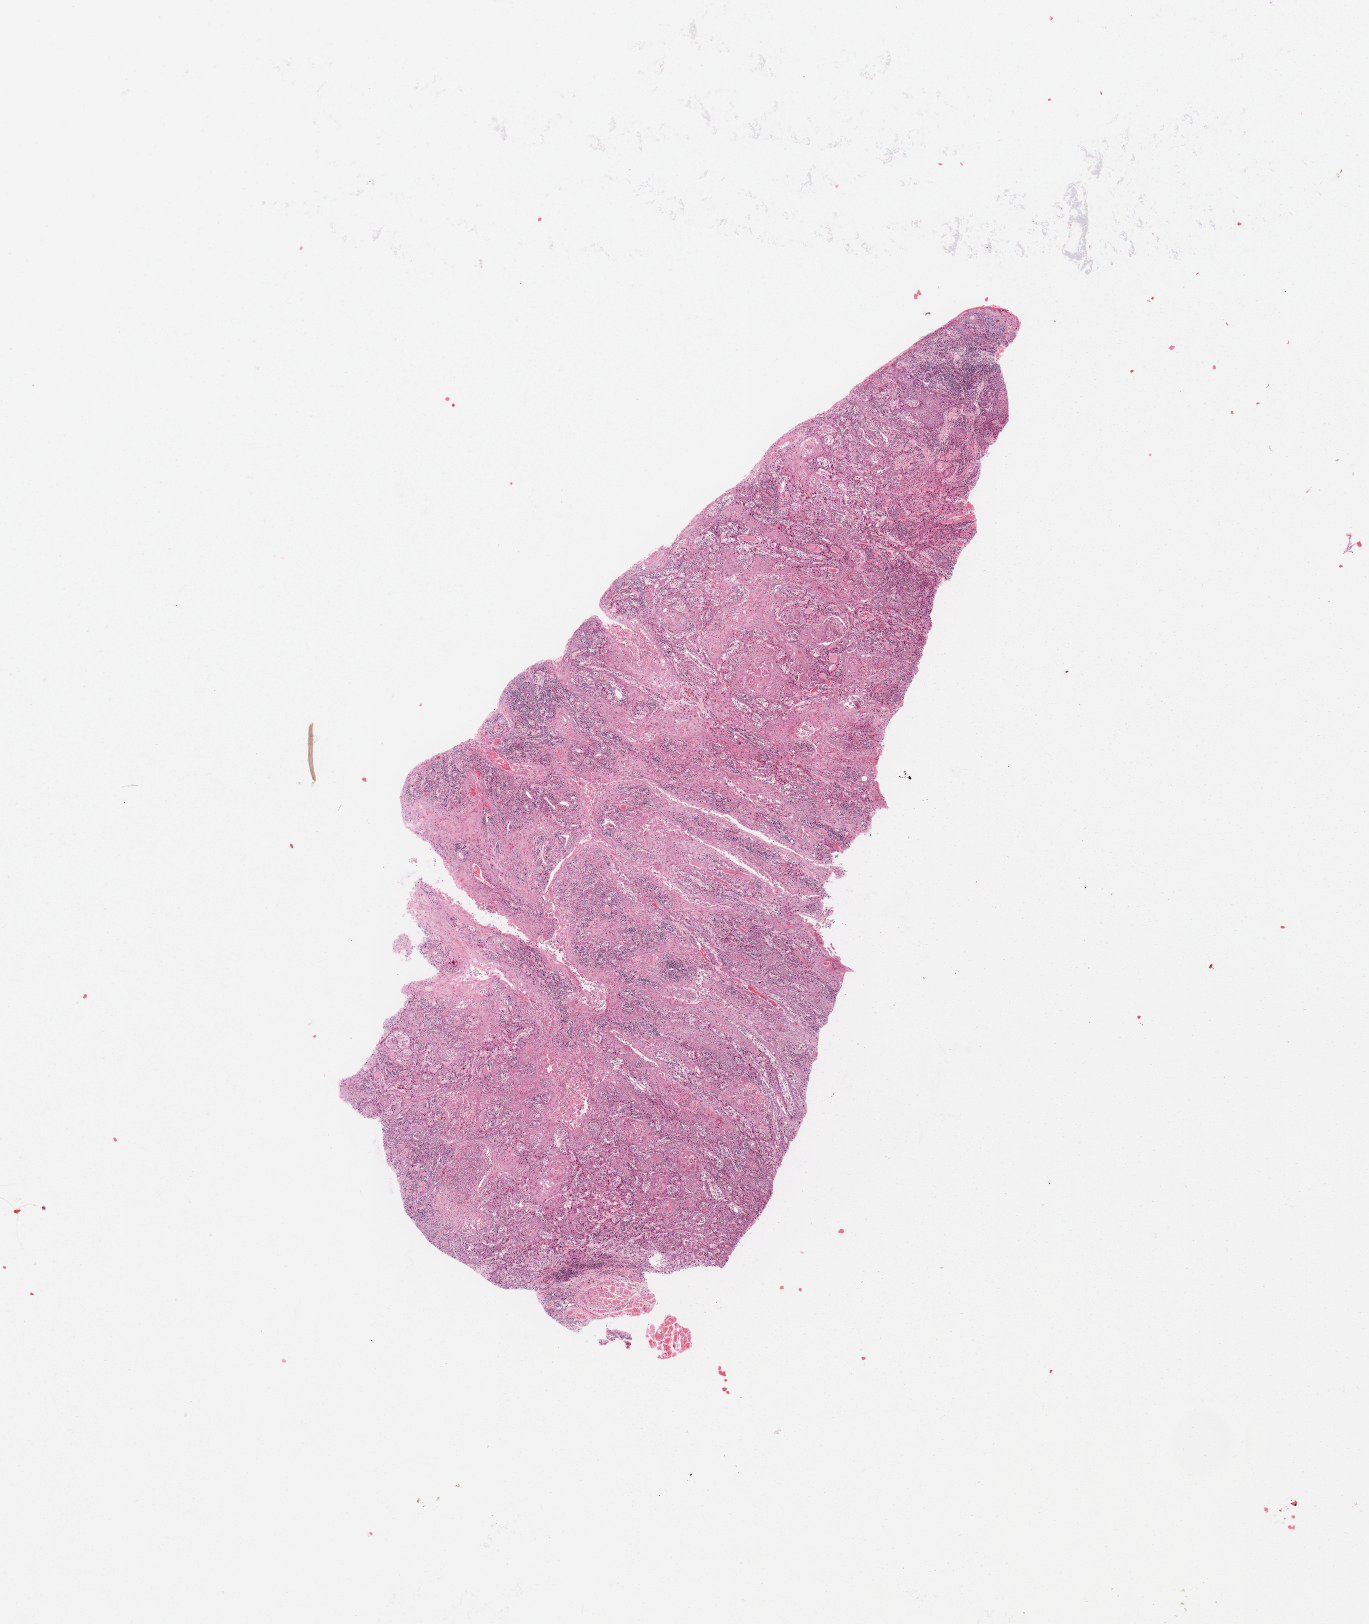
Whole-slide histology image, Hematoxylin and eosin (H&E) stained, low-resolution overview of the scanned area, about 10.8 x 12.8 mm (acquisition: 20x scan). Head and neck, tissue type not recorded. 68-year-old female patient.
Patient diagnosis: Squamous cell carcinoma, NOS (tongue, NOS).